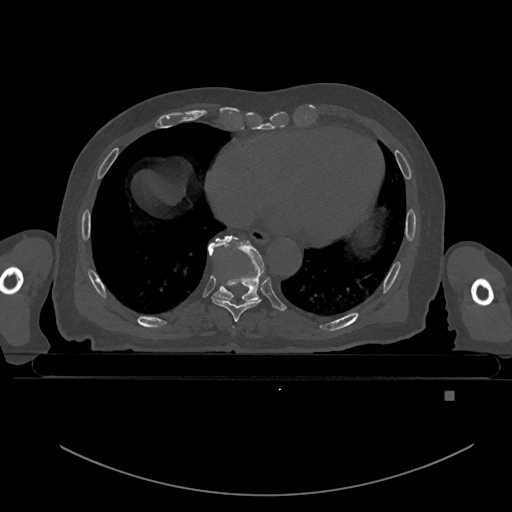
CT including the spine, one axial slice. Slice 179 of 969 in the series (ordered by position). Bone window (W 1800 / L 400 HU). 0.5 mm slice thickness. 512 × 512 image matrix, field of view 456 × 456 mm. Male patient, age 82 years. Case-level facts recorded for this patient, not image findings: primary cancer: prostate; vertebrae with lytic lesions (as recorded): T11, T9, T8, T2.
Structures marked on this image (semi-automatically segmented with operator editing):
- T7 vertebra: bounding box (x1, y1, x2, y2) in pixels: (232, 327, 234, 329)
- T8 vertebra: (212, 296, 261, 322)
- T9 vertebra: (207, 235, 264, 303)